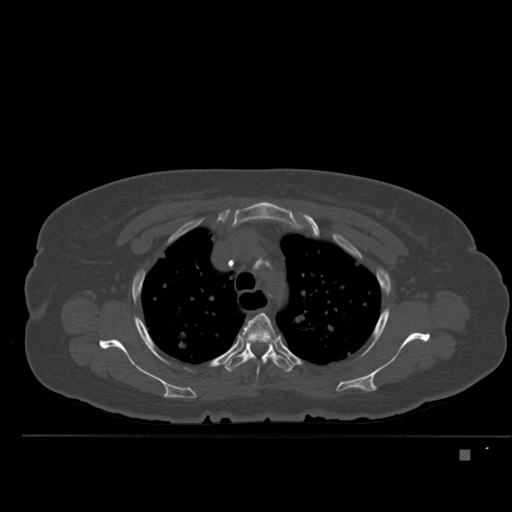
CT including the spine, one axial slice; bone window (W 1800 / L 400 HU); 512 × 512 image matrix. Patient: female, 74 years. From the clinical record (not read from this slice): primary cancer: colon.
Structures marked on this image (semi-automatically segmented with operator editing):
- T3 vertebra: bounding box (x1, y1, x2, y2) in pixels: (240, 313, 279, 376)
- T4 vertebra: (224, 341, 293, 373)